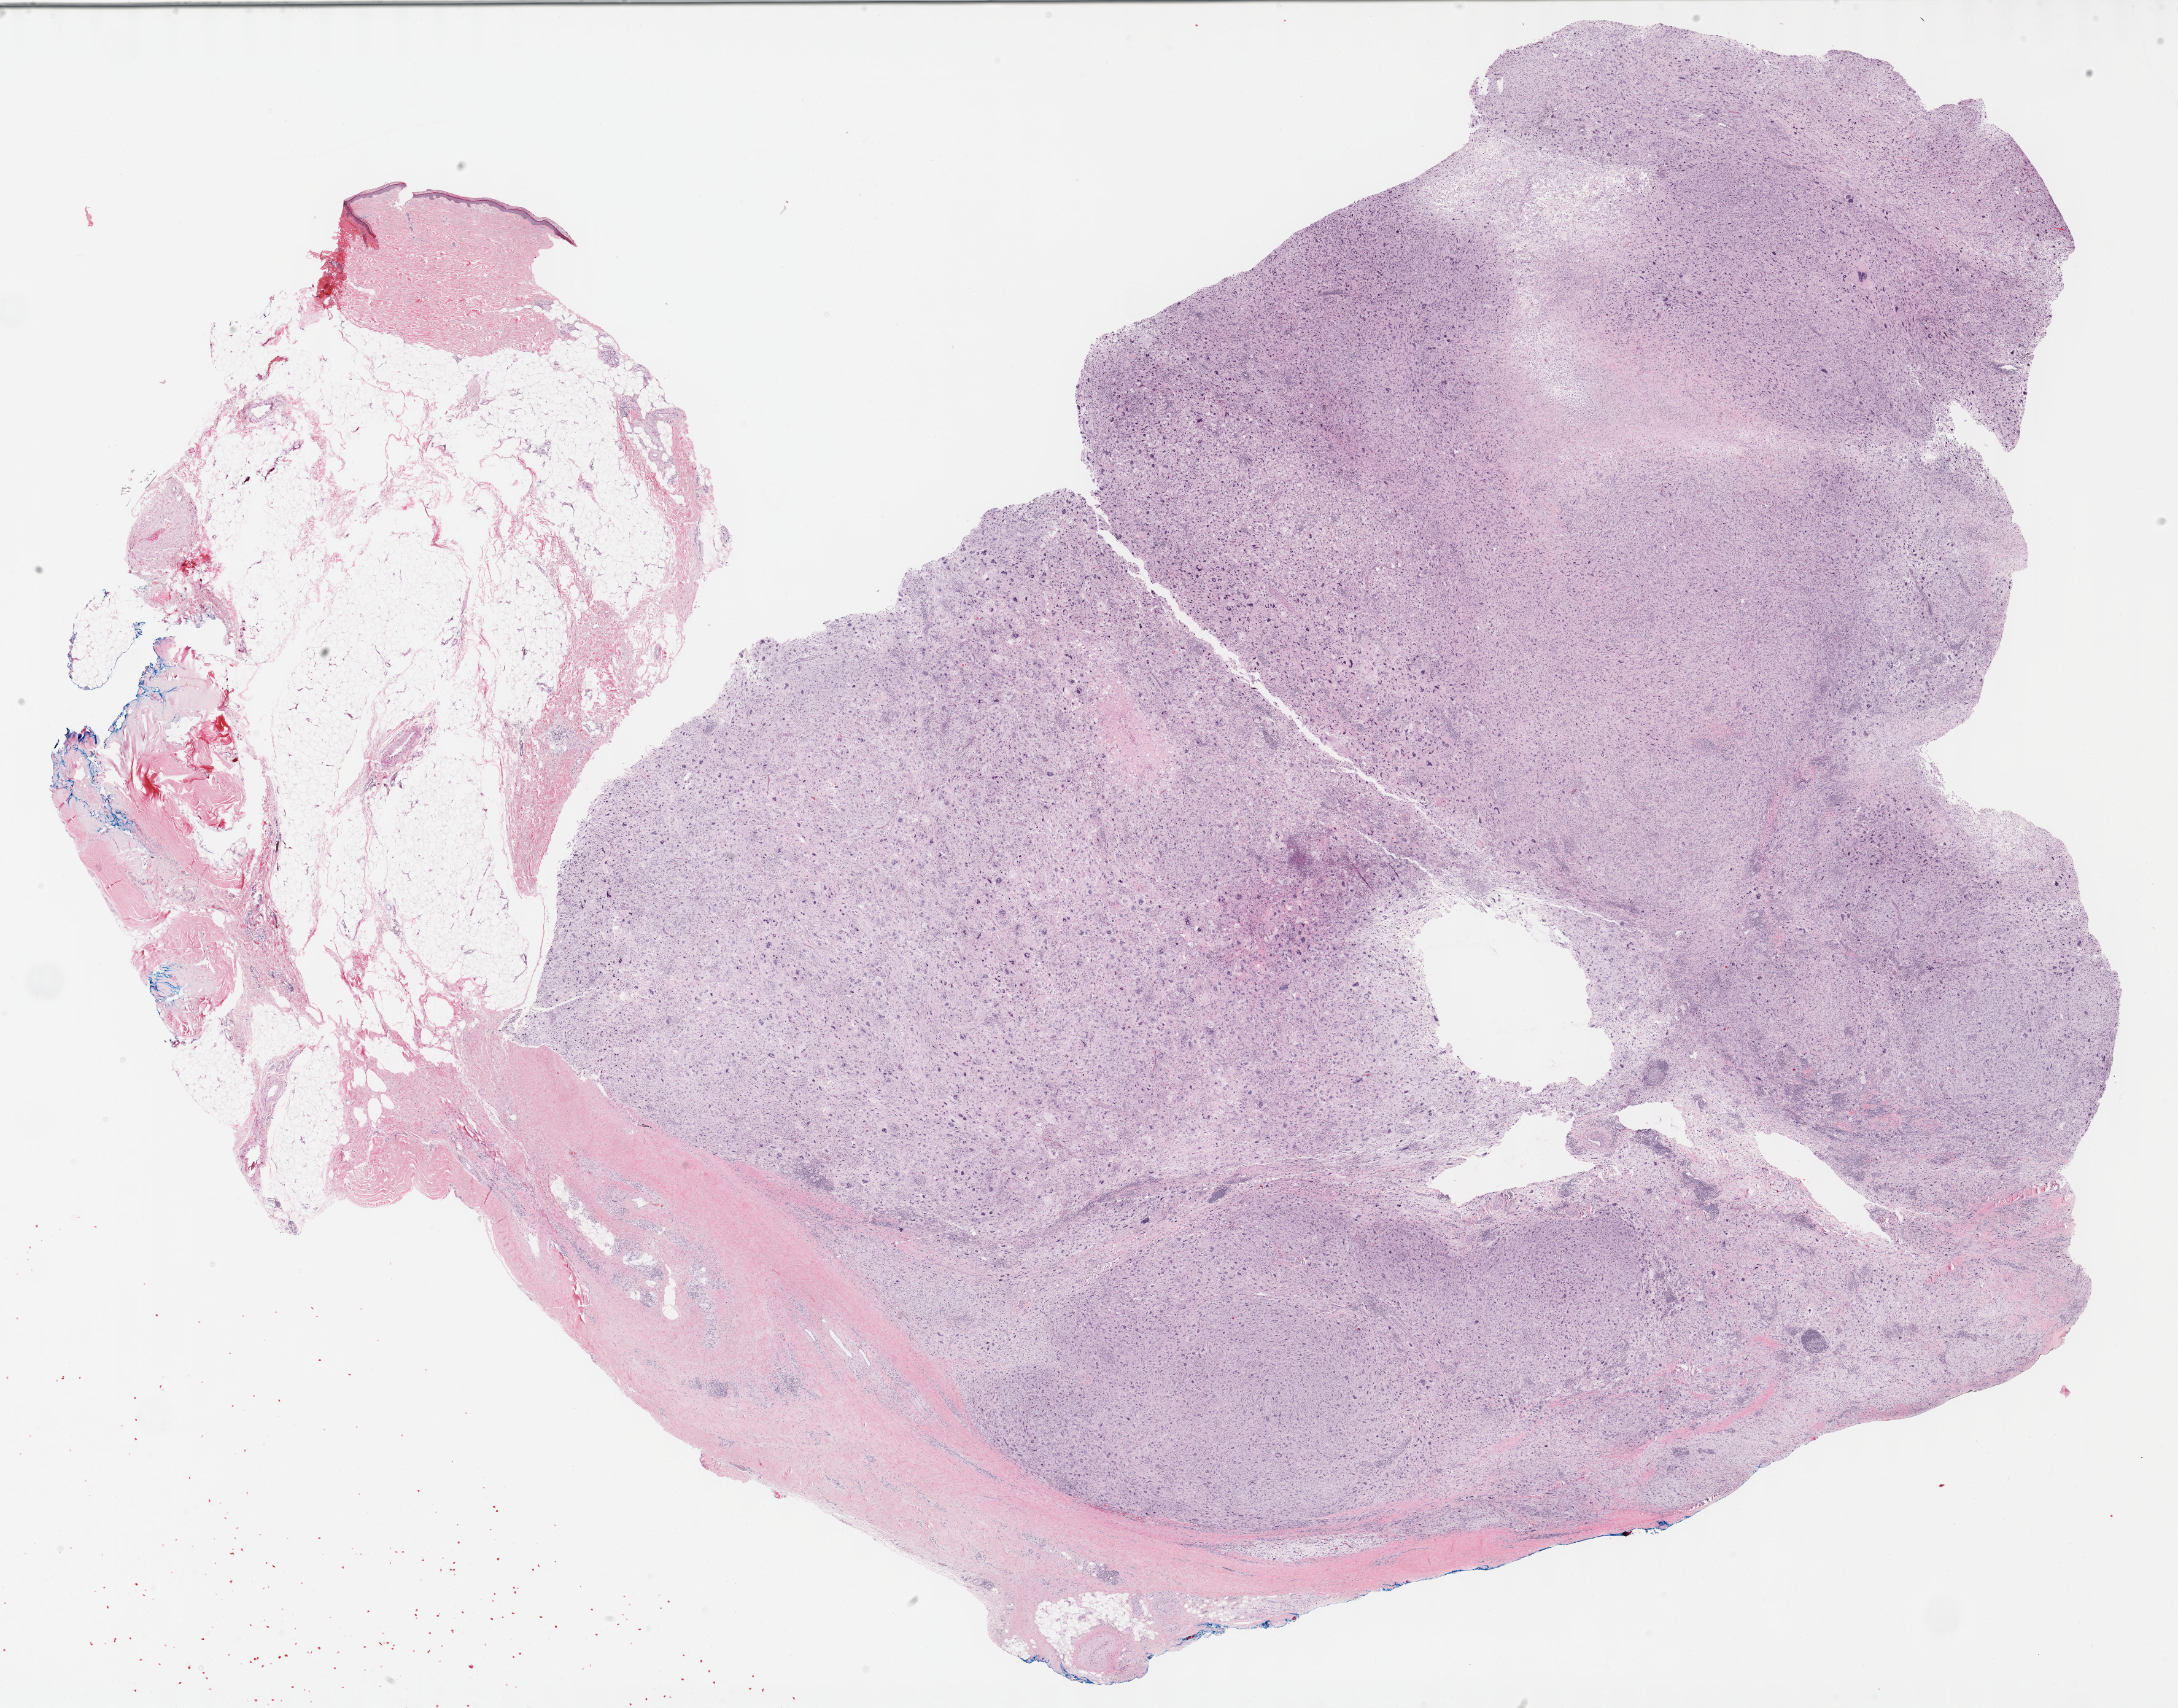
Whole-slide histology image, H&E-stained — a low-resolution overview of the entire scanned area, about 28.7 x 22.5 mm, FFPE section, sample: primary tumour, connective, subcutaneous and other soft tissues. Female patient; age at initial diagnosis 67 years.
- pathologic diagnosis: Undifferentiated sarcoma